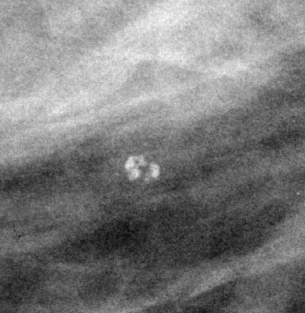
Region of interest cut from a scanned film mammogram (one marked finding), right breast, MLO view, BI-RADS breast density category 2 (scale 1–4).
Finding: calcifications, morphology pleomorphic, distribution clustered; BI-RADS assessment category 3; pathology (as recorded): benign.